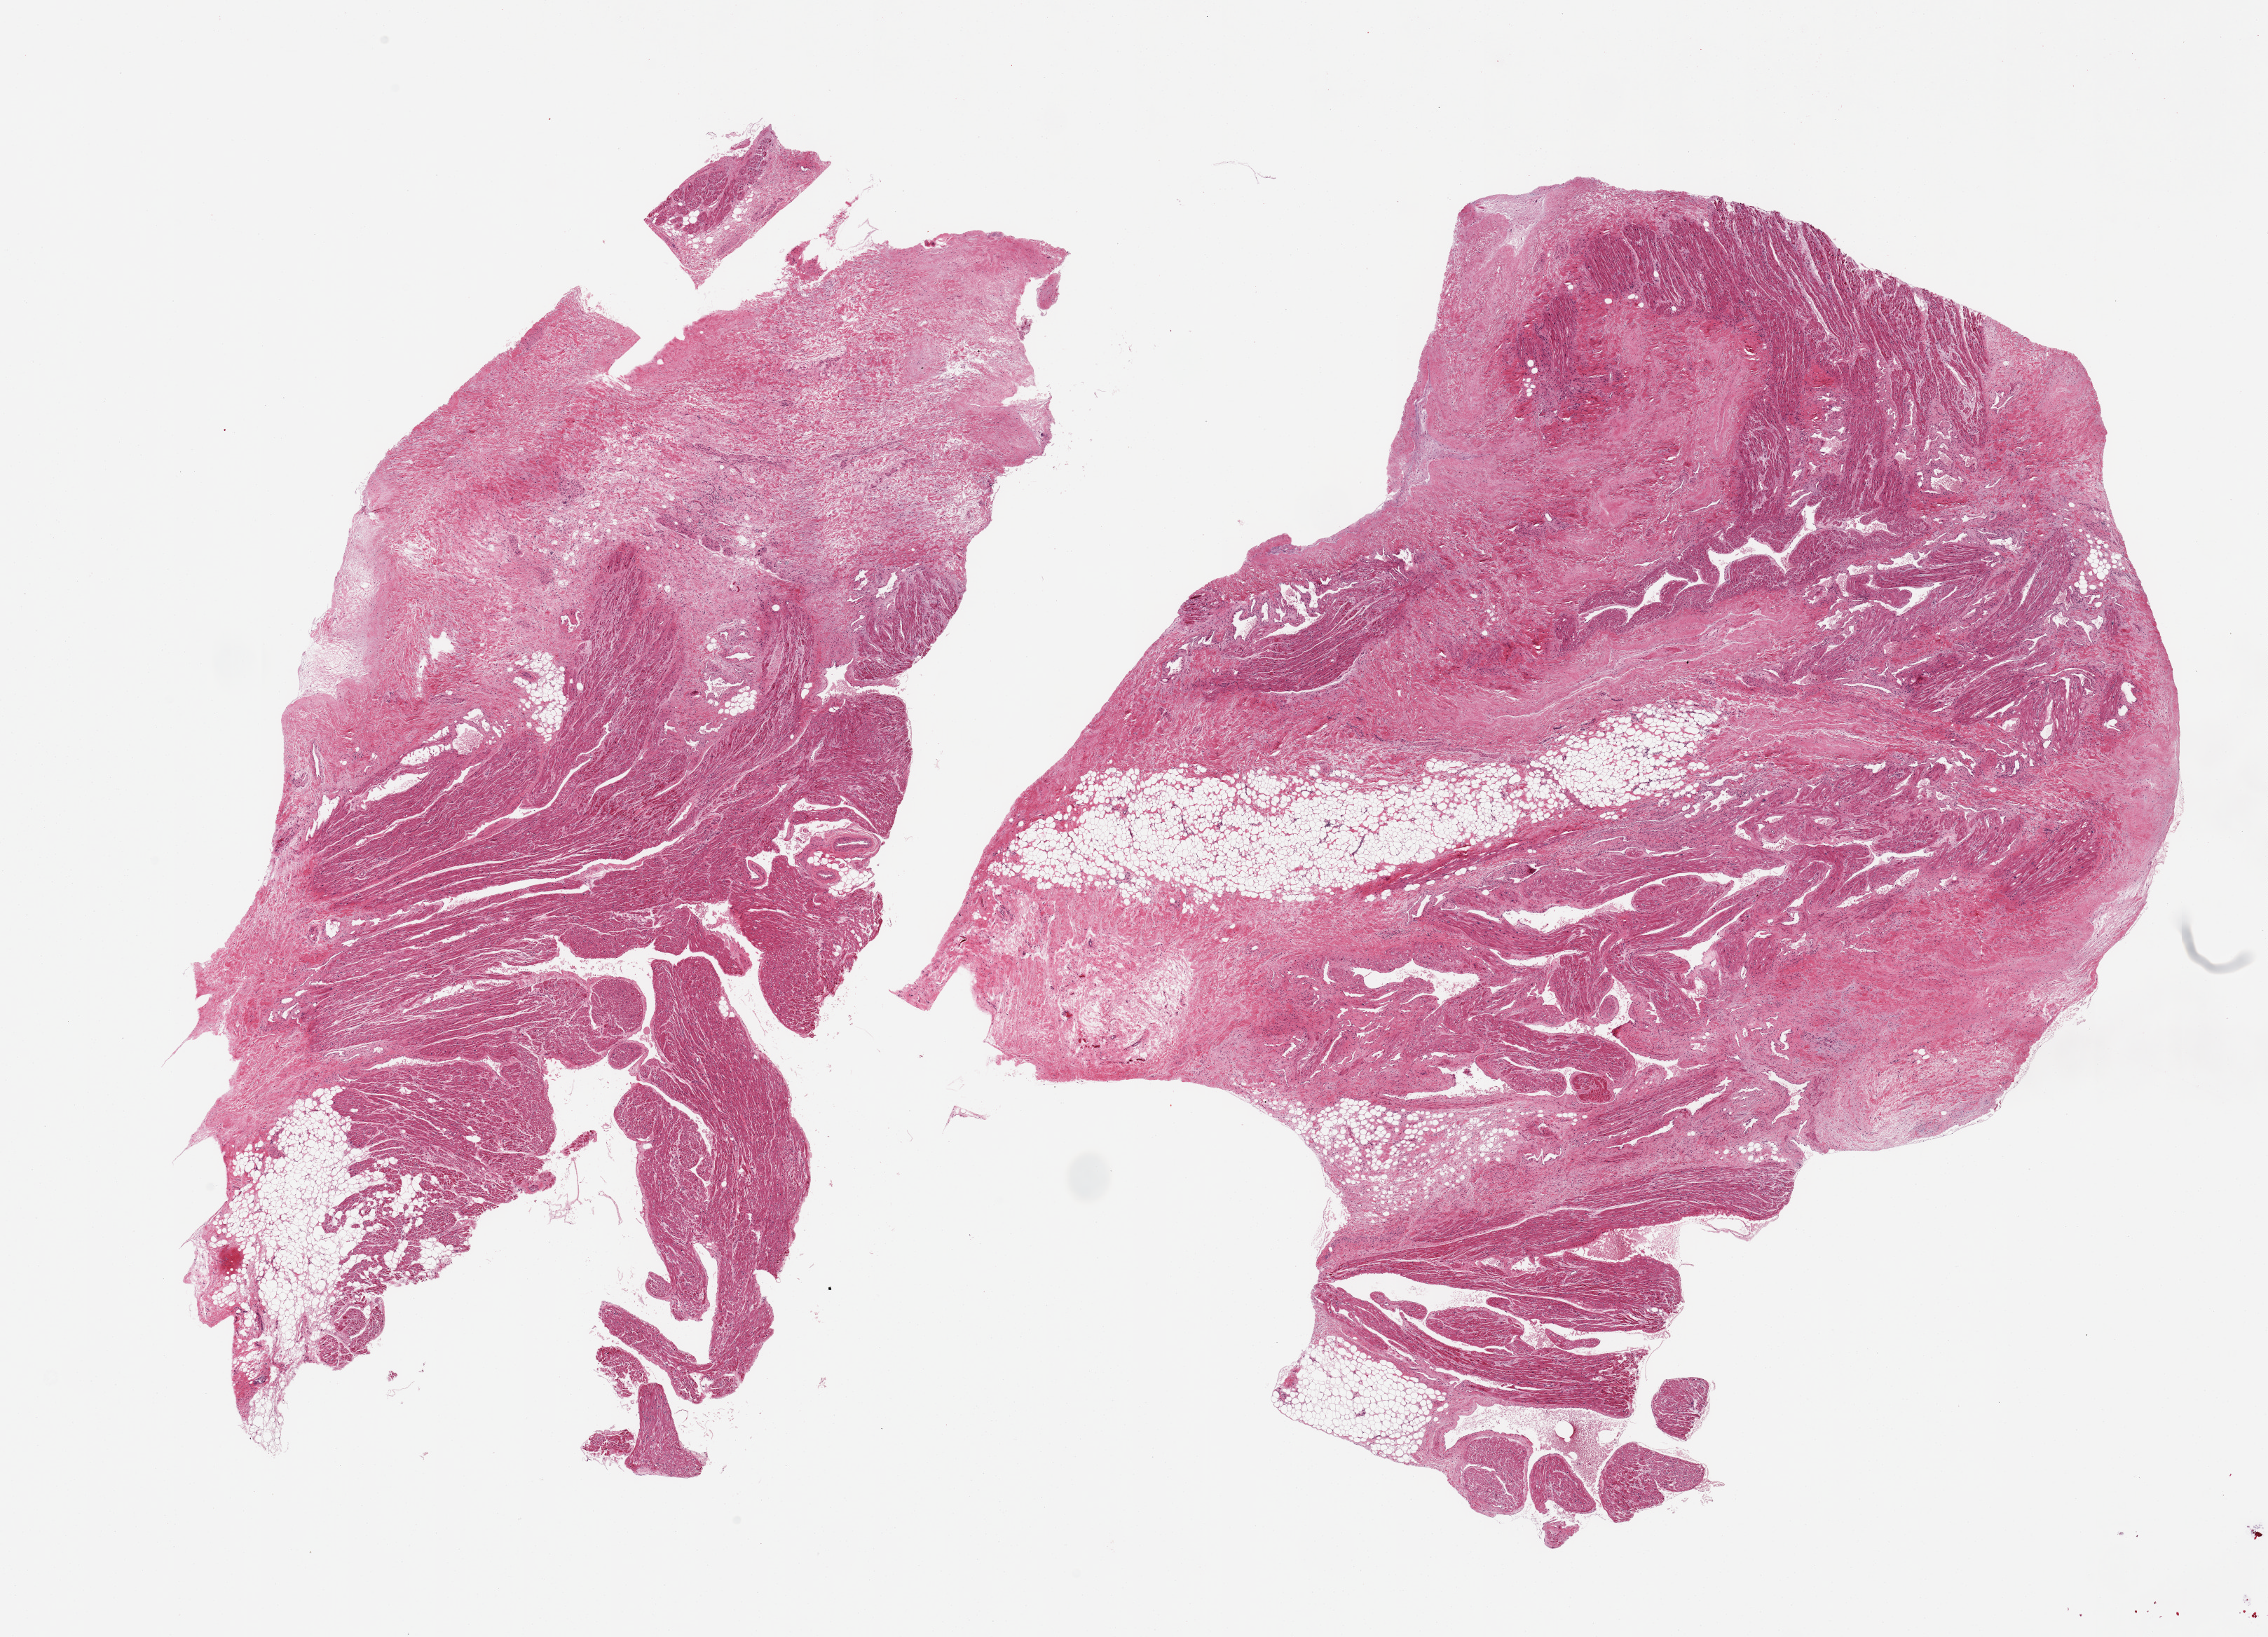
Hematoxylin and eosin (H&E) whole-slide image, brightfield, a low-resolution overview of the entire scanned area, about 25.6 x 18.5 mm (acquisition: 20x scan). PAXgene-fixed, paraffin-embedded tissue. Sampled site (target tissue): auricular appendage. Donor tissue sample. Donor: female.
* pathologist's review note for this sample: 2 pieces, no abnormalities